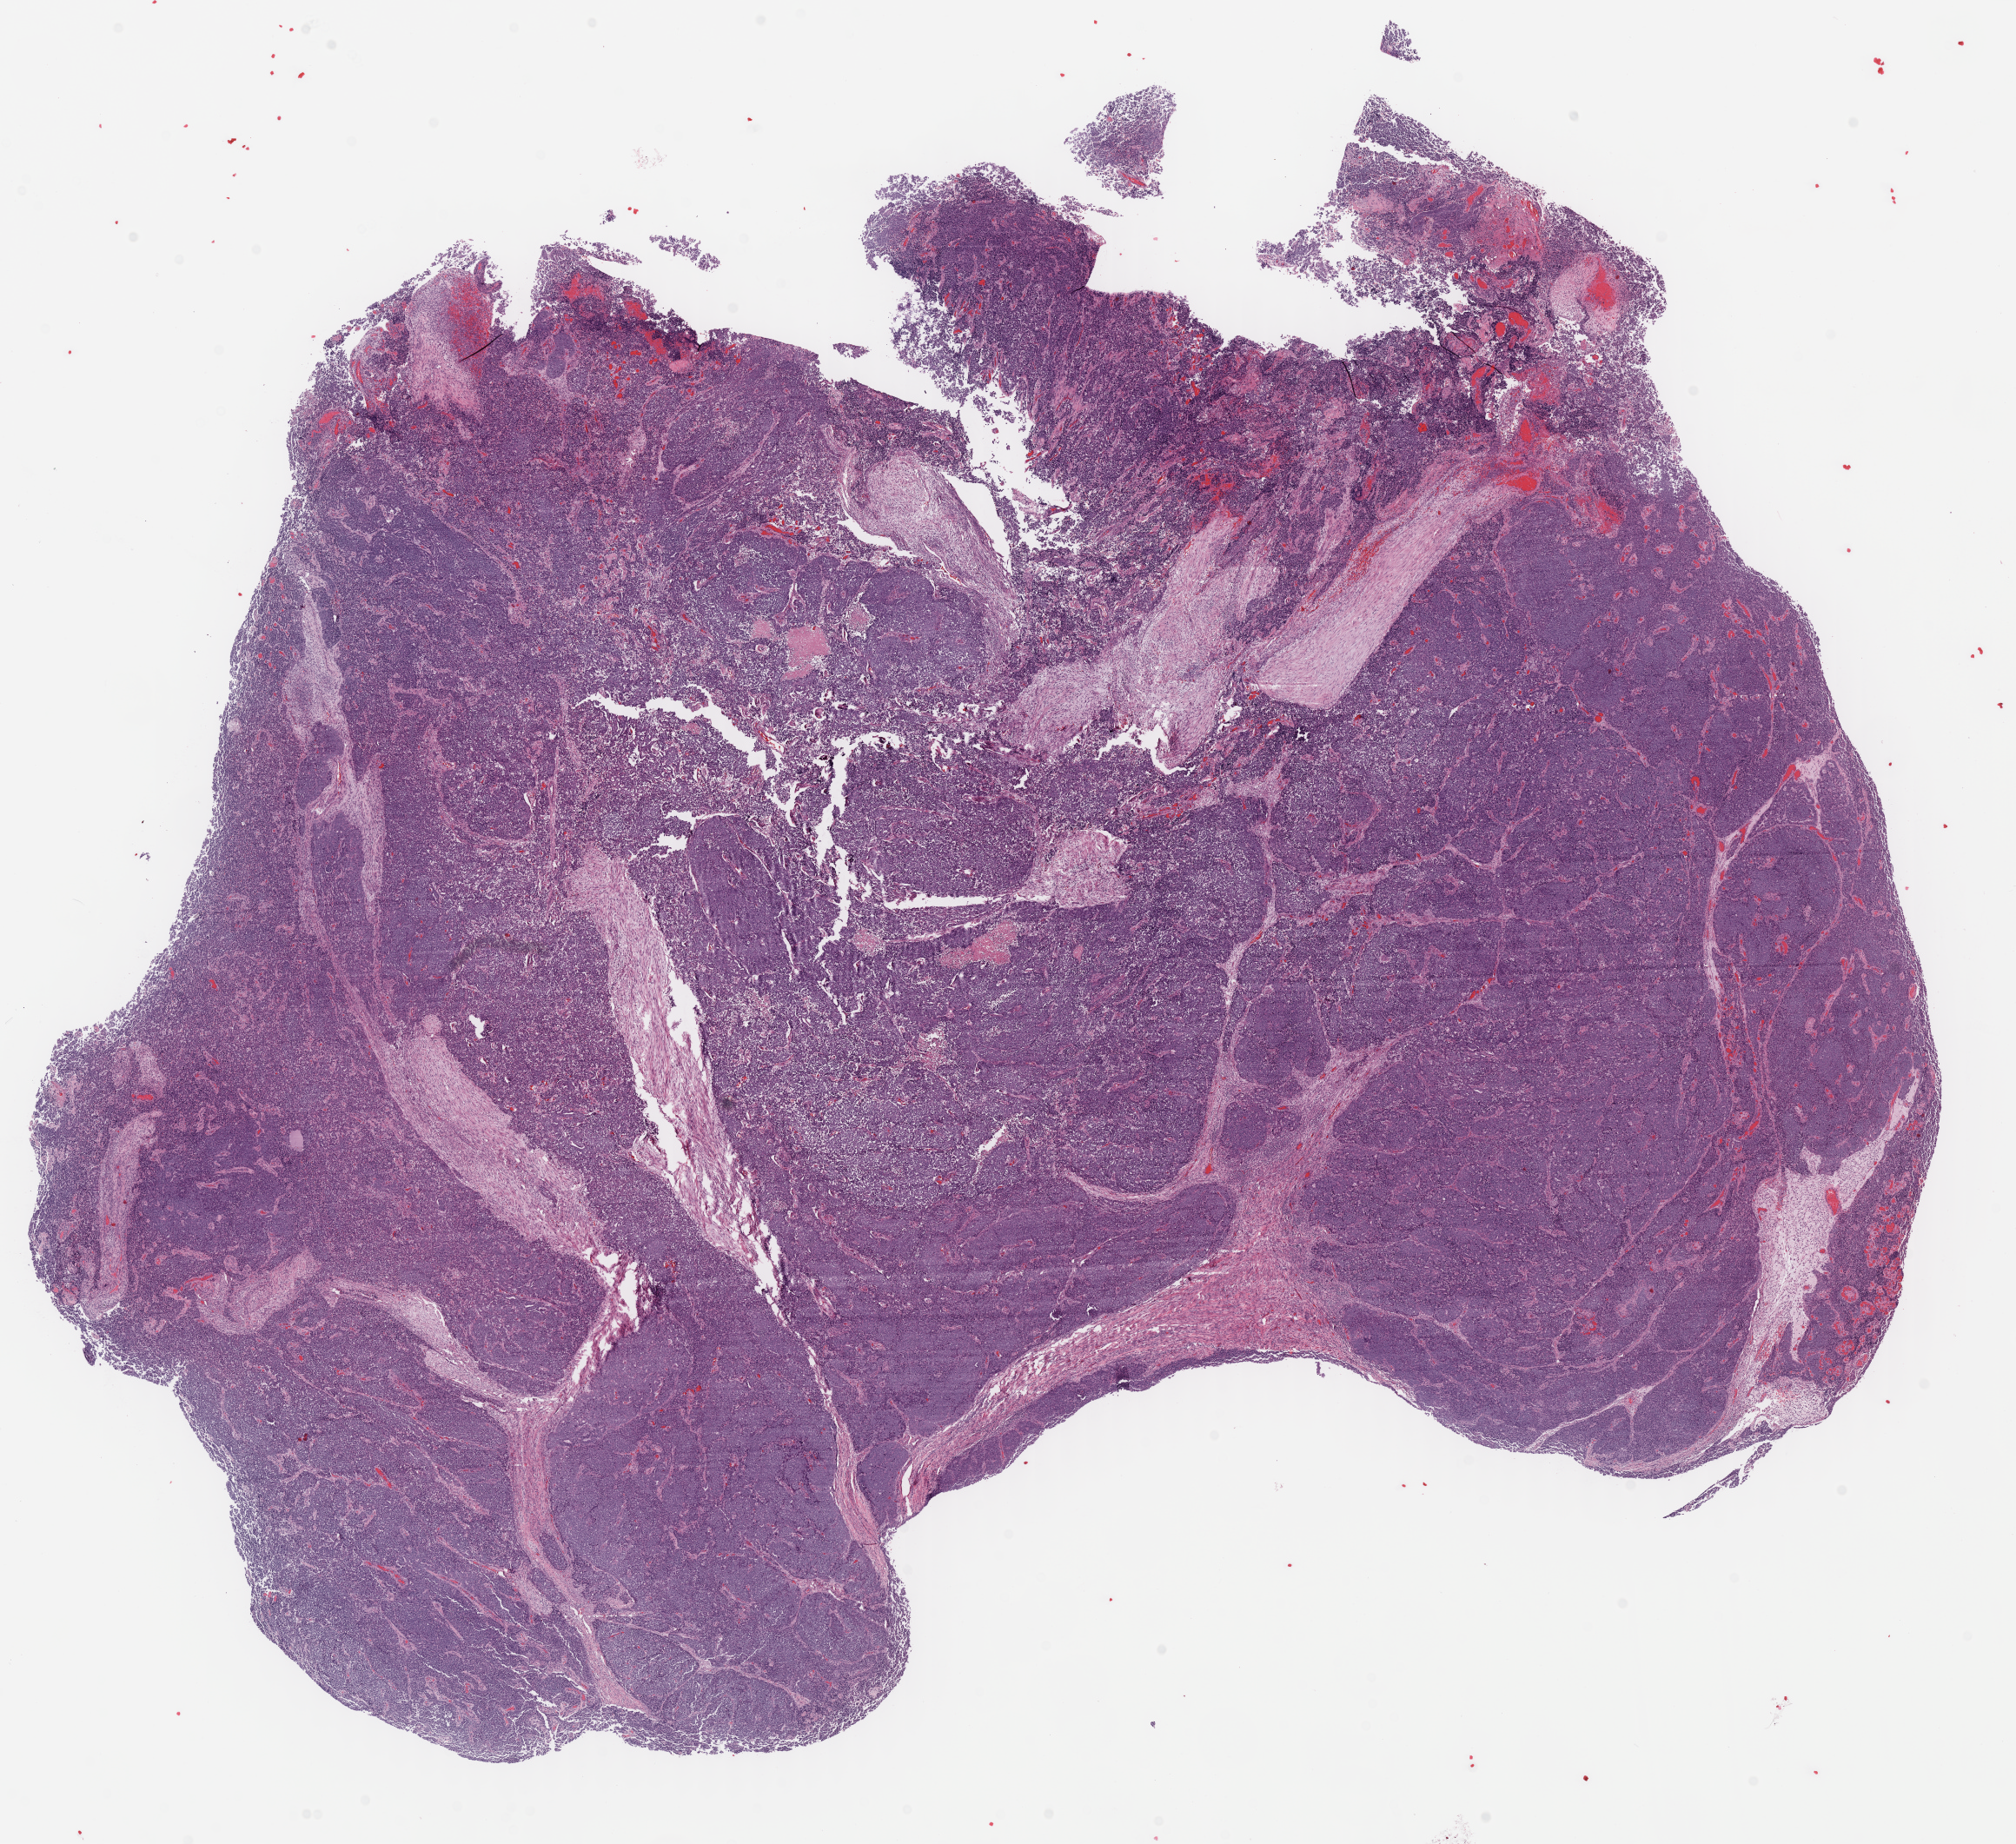
H&E-stained whole-slide image — low-resolution overview of the scanned area, about 18.4 x 16.8 mm (from a 40x scan); formalin-fixed paraffin-embedded (FFPE) diagnostic section; primary tumour sample from the uterus. Female, age 82 years at initial diagnosis. Histologic grade: G3 (poorly differentiated).
- FIGO stage: IA
- pathologic diagnosis: Endometrioid adenocarcinoma, NOS